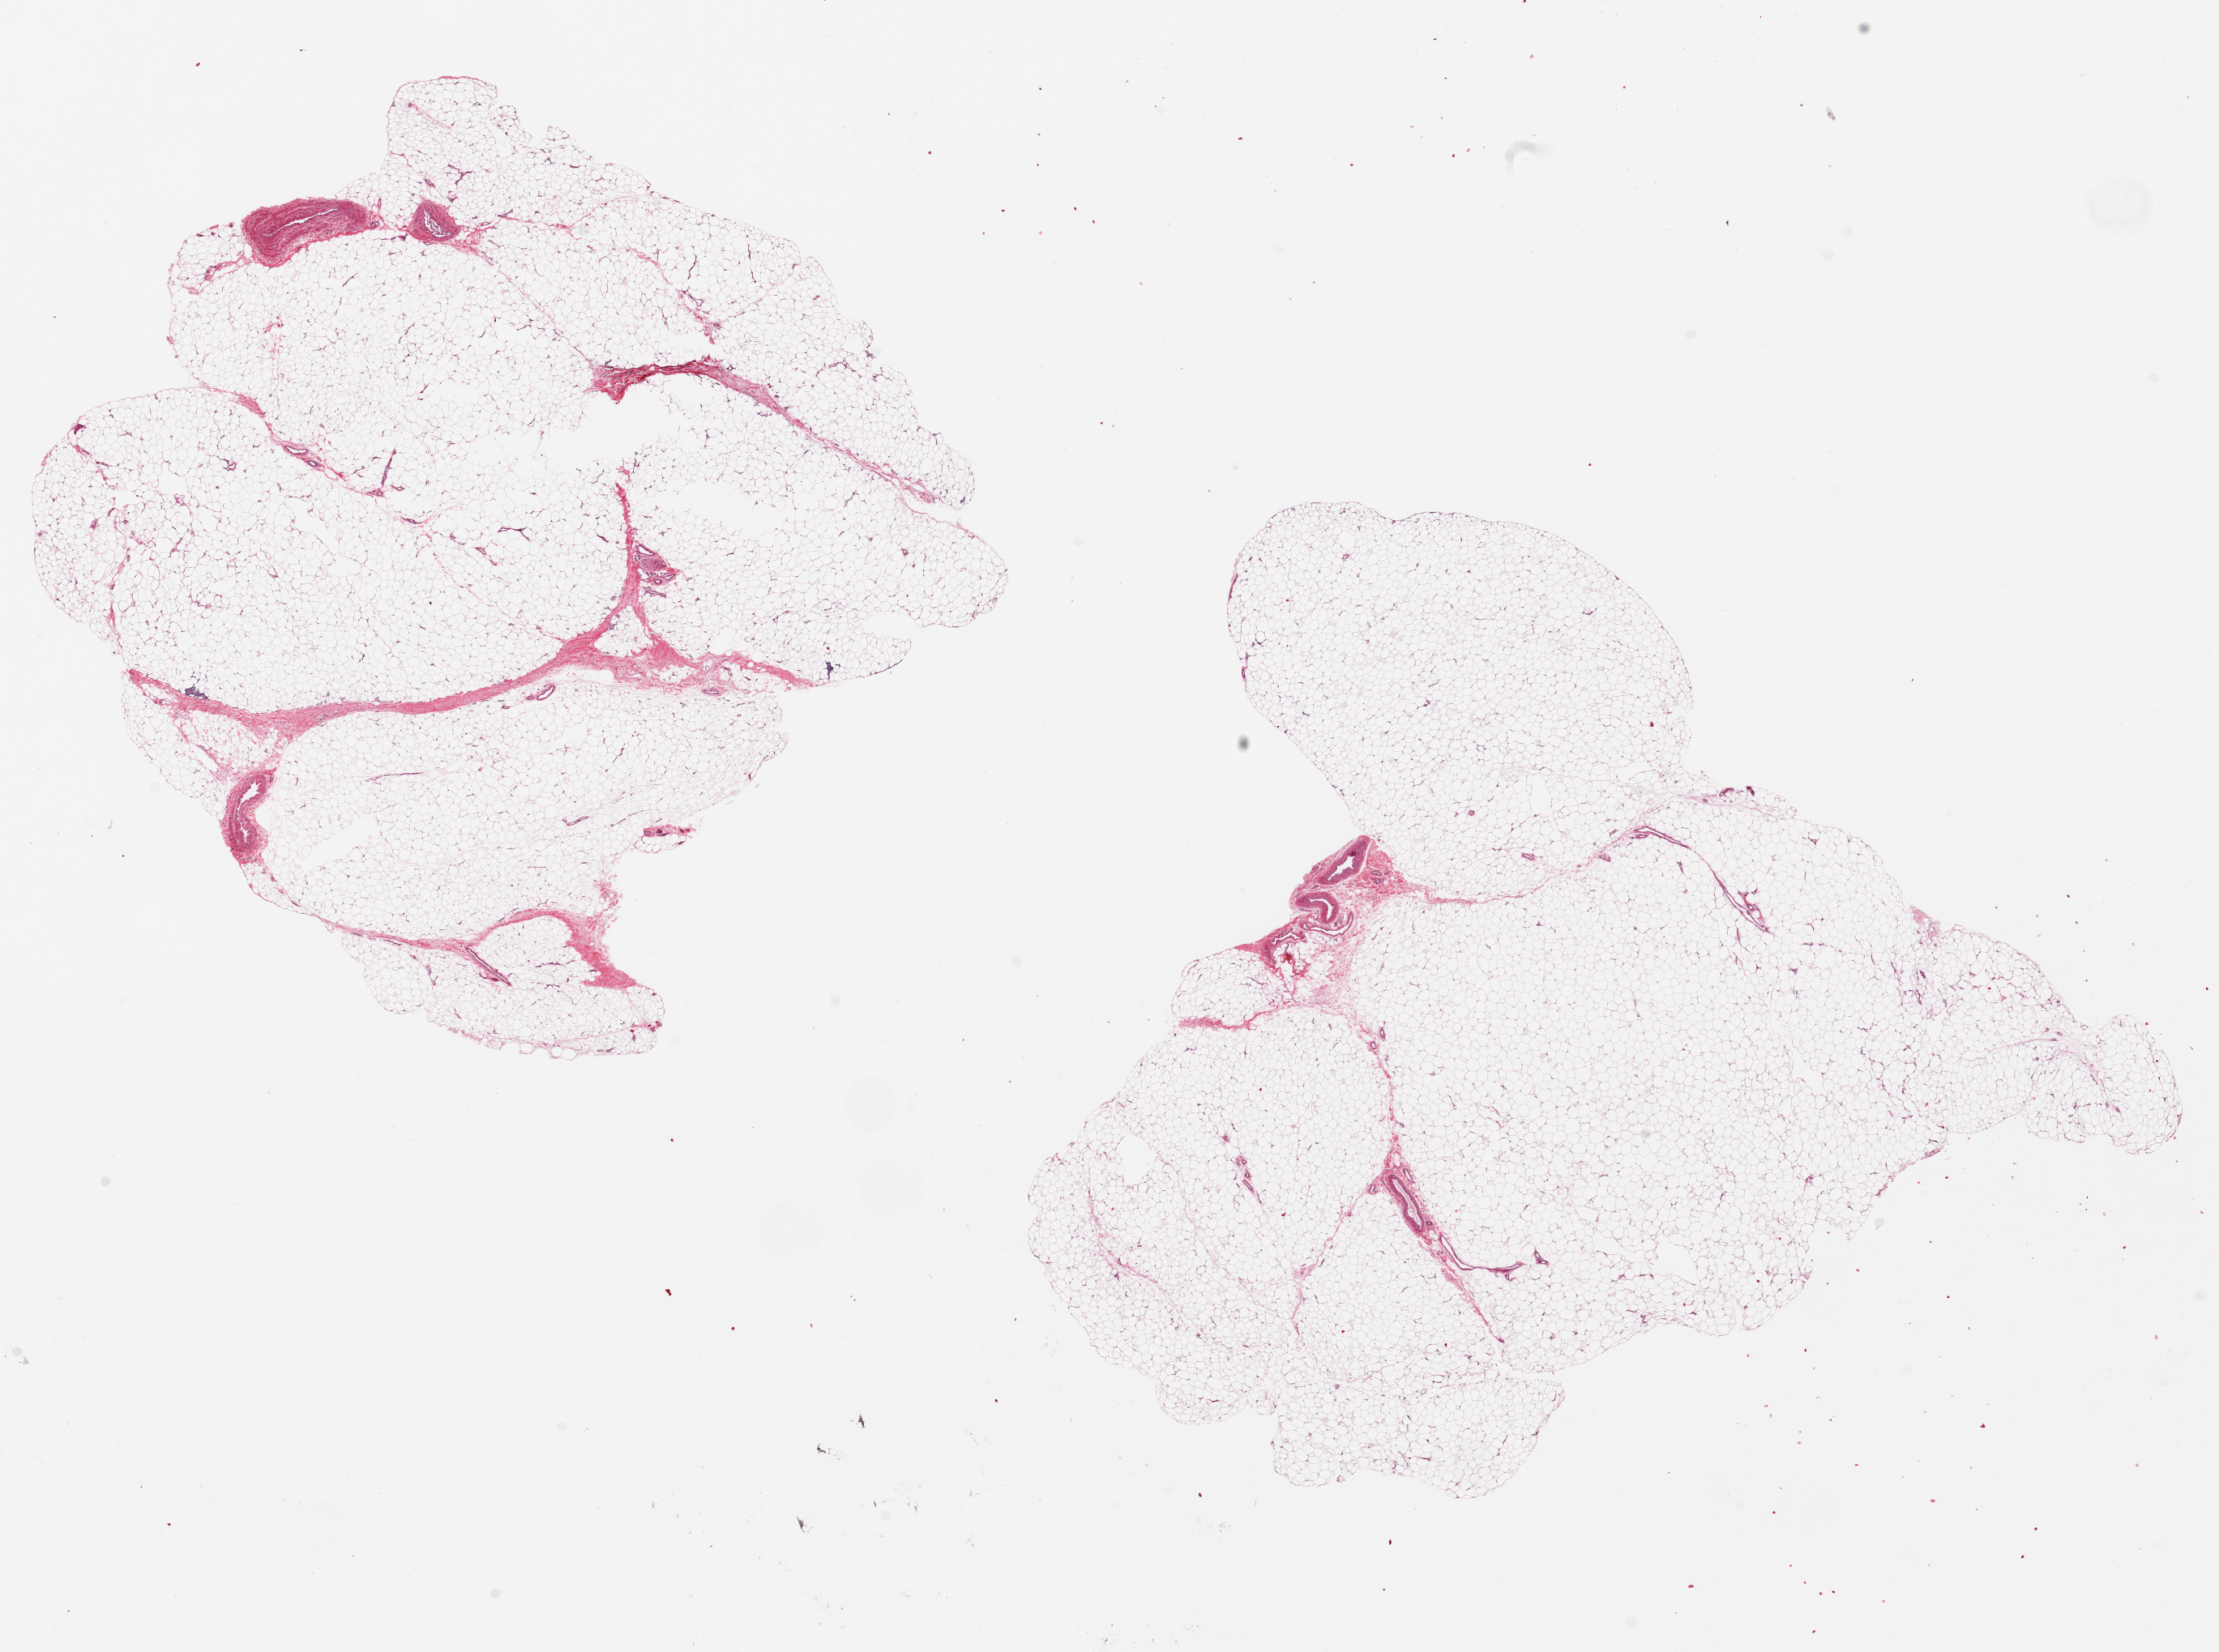
H&E whole-slide image, shown as a low-resolution overview of the whole scanned area (about 21.7 x 16.1 mm, slide scanned at 20x). PAXgene-fixed, paraffin-embedded tissue. Section of adipose tissue (target tissue). Tissue donor sample. Male donor.
Pathologist's review note for this sample: 2 ~8.5x8mm aliquots.